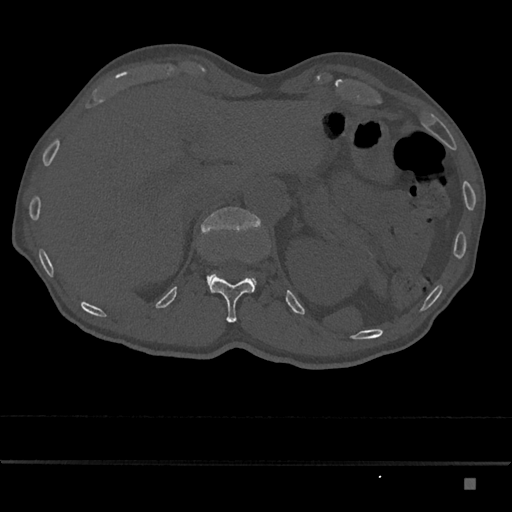
CT including the spine, one axial slice. Position 592 of 797 along the scan axis. Reconstruction kernel Br40s/3. 120 kVp. Bone window (W 1800 / L 400 HU). 0.5 mm slice thickness. 512 × 512 image matrix, field of view 390 × 390 mm. Male patient, age 72 years. From the clinical record (not read from this slice): primary cancer: prostate.
Annotated regions visible in this slice (semi-automatically segmented with operator editing):
- L1 vertebra: bounding box <201,207,261,290> (left, top, right, bottom; pixels)
- T12 vertebra: <210,276,255,323>